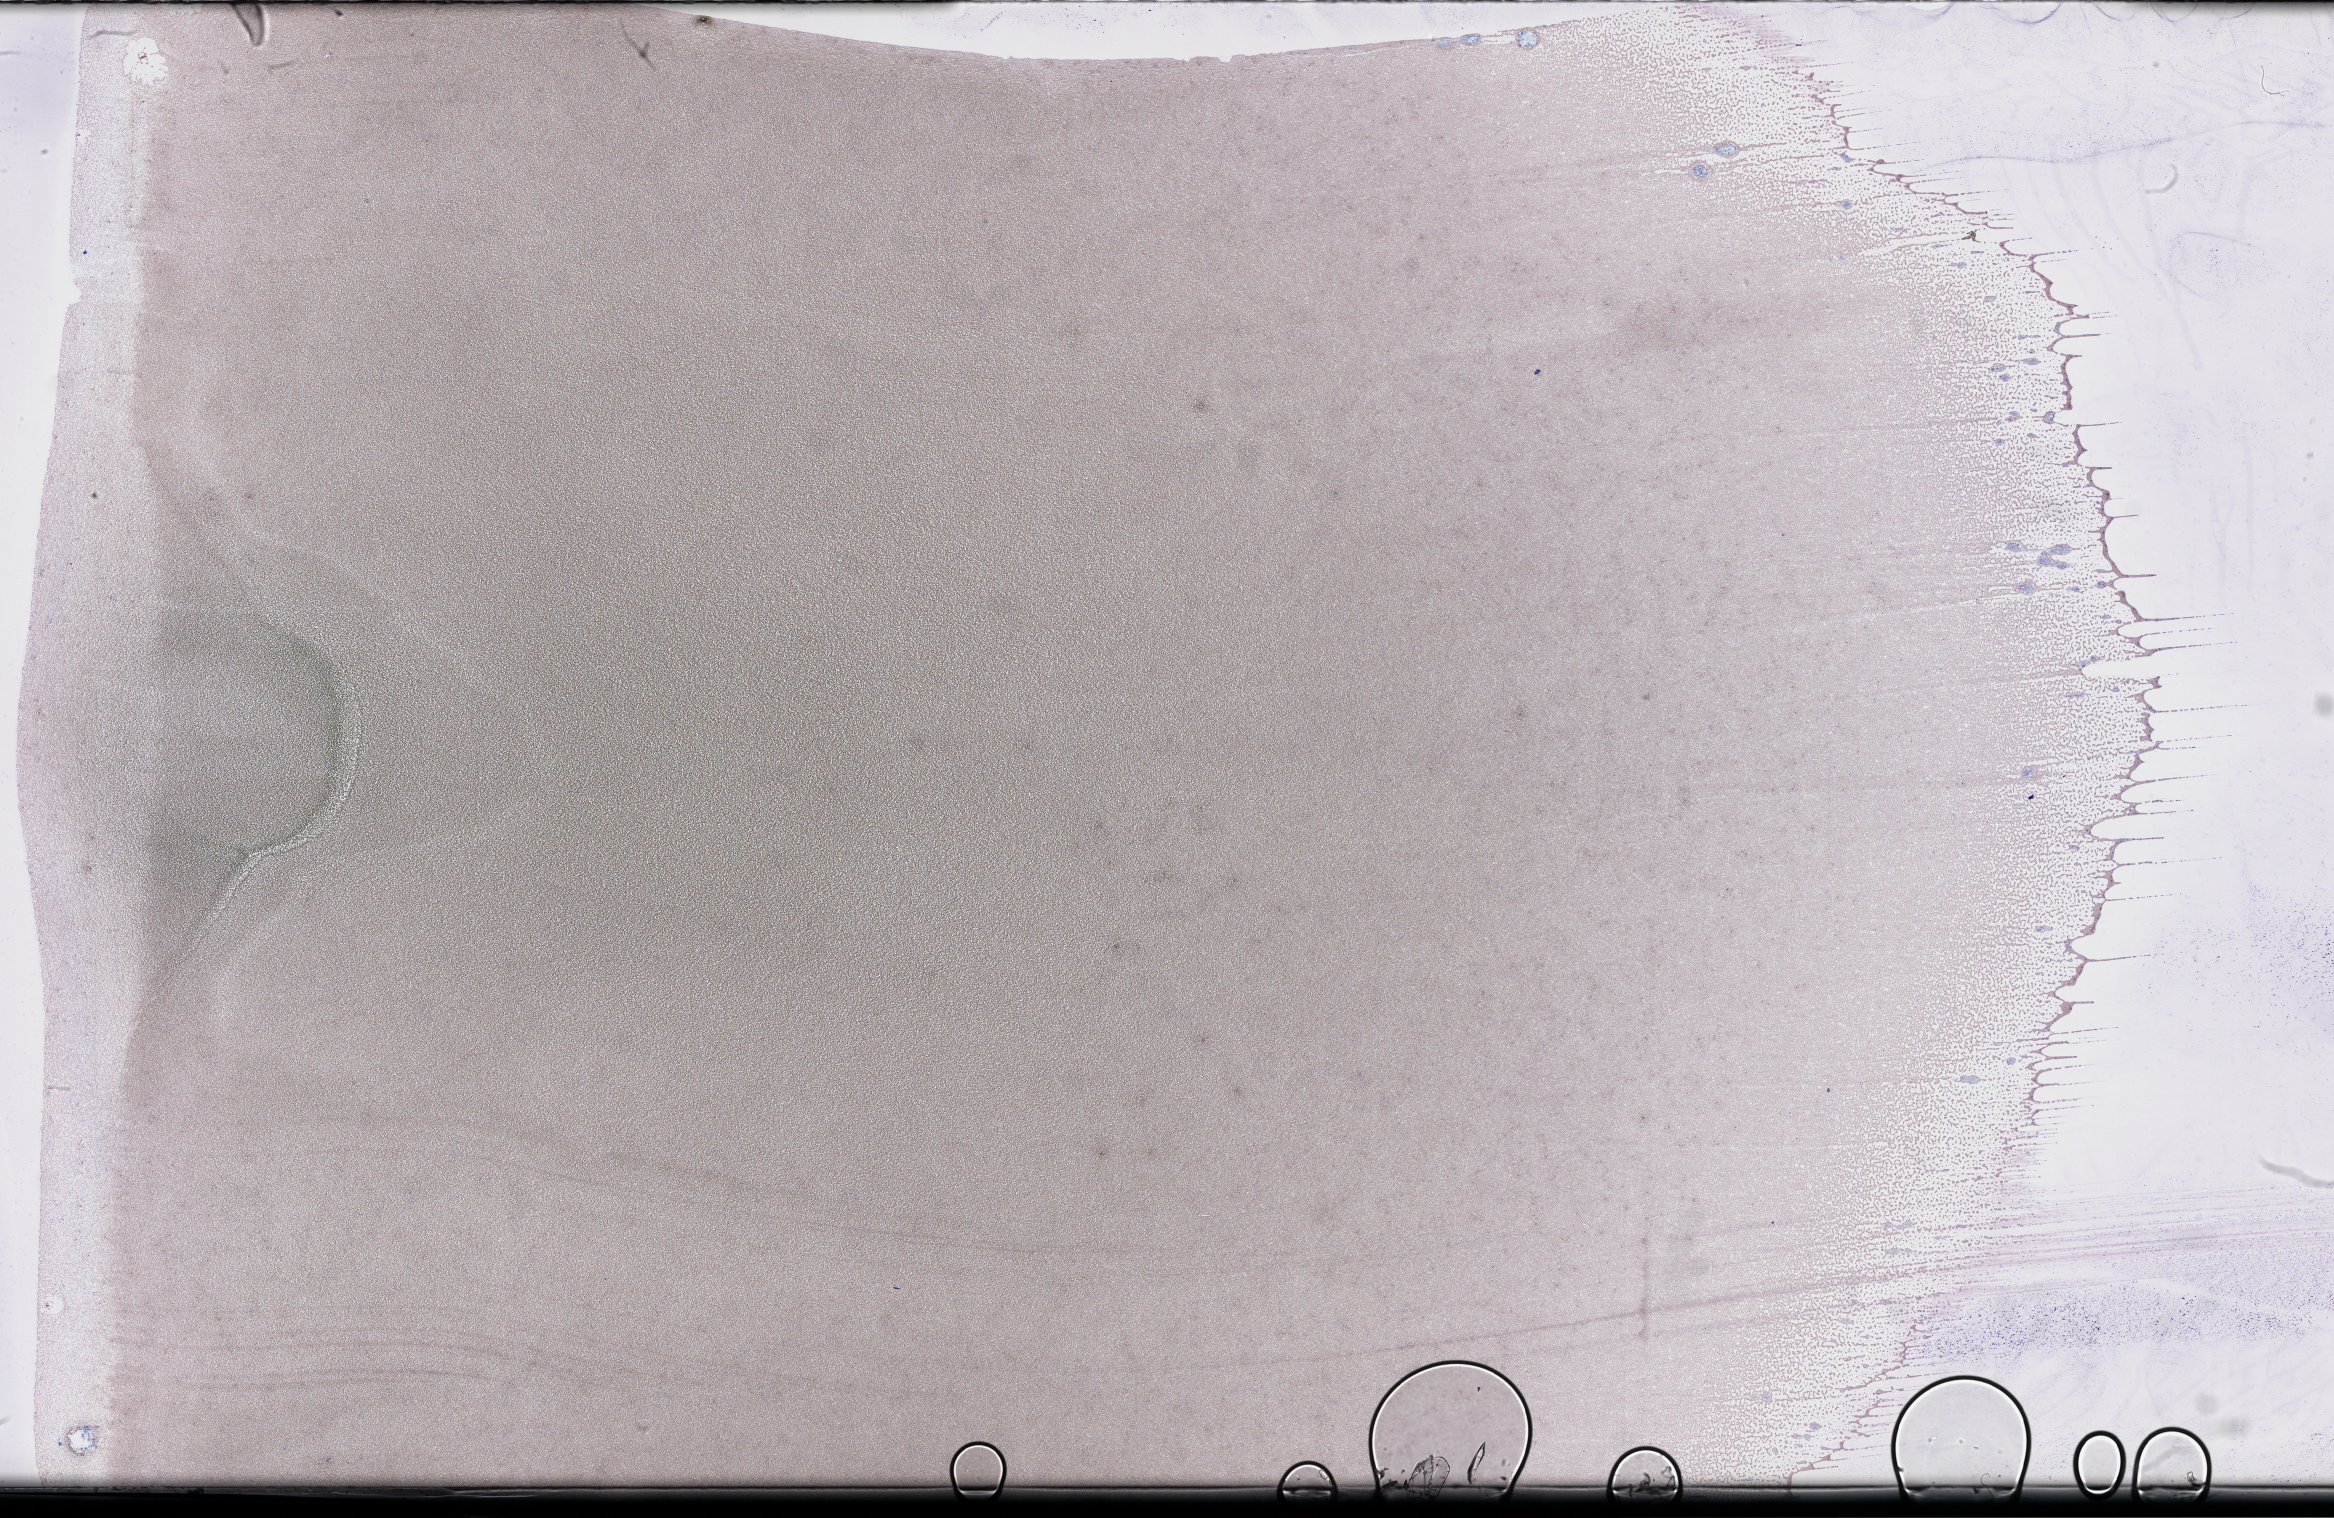
Whole-slide image of a whole blood smear, Wright-Giemsa stain, whole scanned area (about 37.7 x 24.5 mm) shown as a low-resolution overview. Collected on treatment. Patient: male.
From a patient with: Plasma Cell Myeloma.